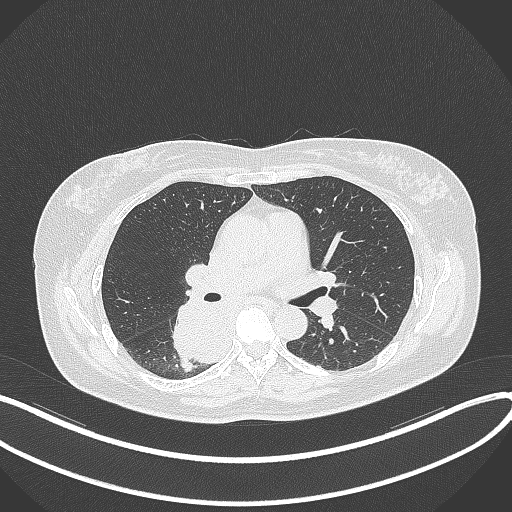
Chest CT, one axial slice; slice 208 of 331 in the series (ordered by position); reconstruction kernel B70f; lung window (W 1500 / L -600 HU); 1 mm slice thickness; 512 × 512 image matrix, field of view 400 × 400 mm. Female patient, age 54 years. From the clinical record (not read from this slice): clinical TNM (as recorded): T4 N0 M0.
Outlined on this slice (bounding box drawn by a radiologist):
- lung tumour (recorded histology: adenocarcinoma): bounding box <166,299,231,365> (left, top, right, bottom; pixels)